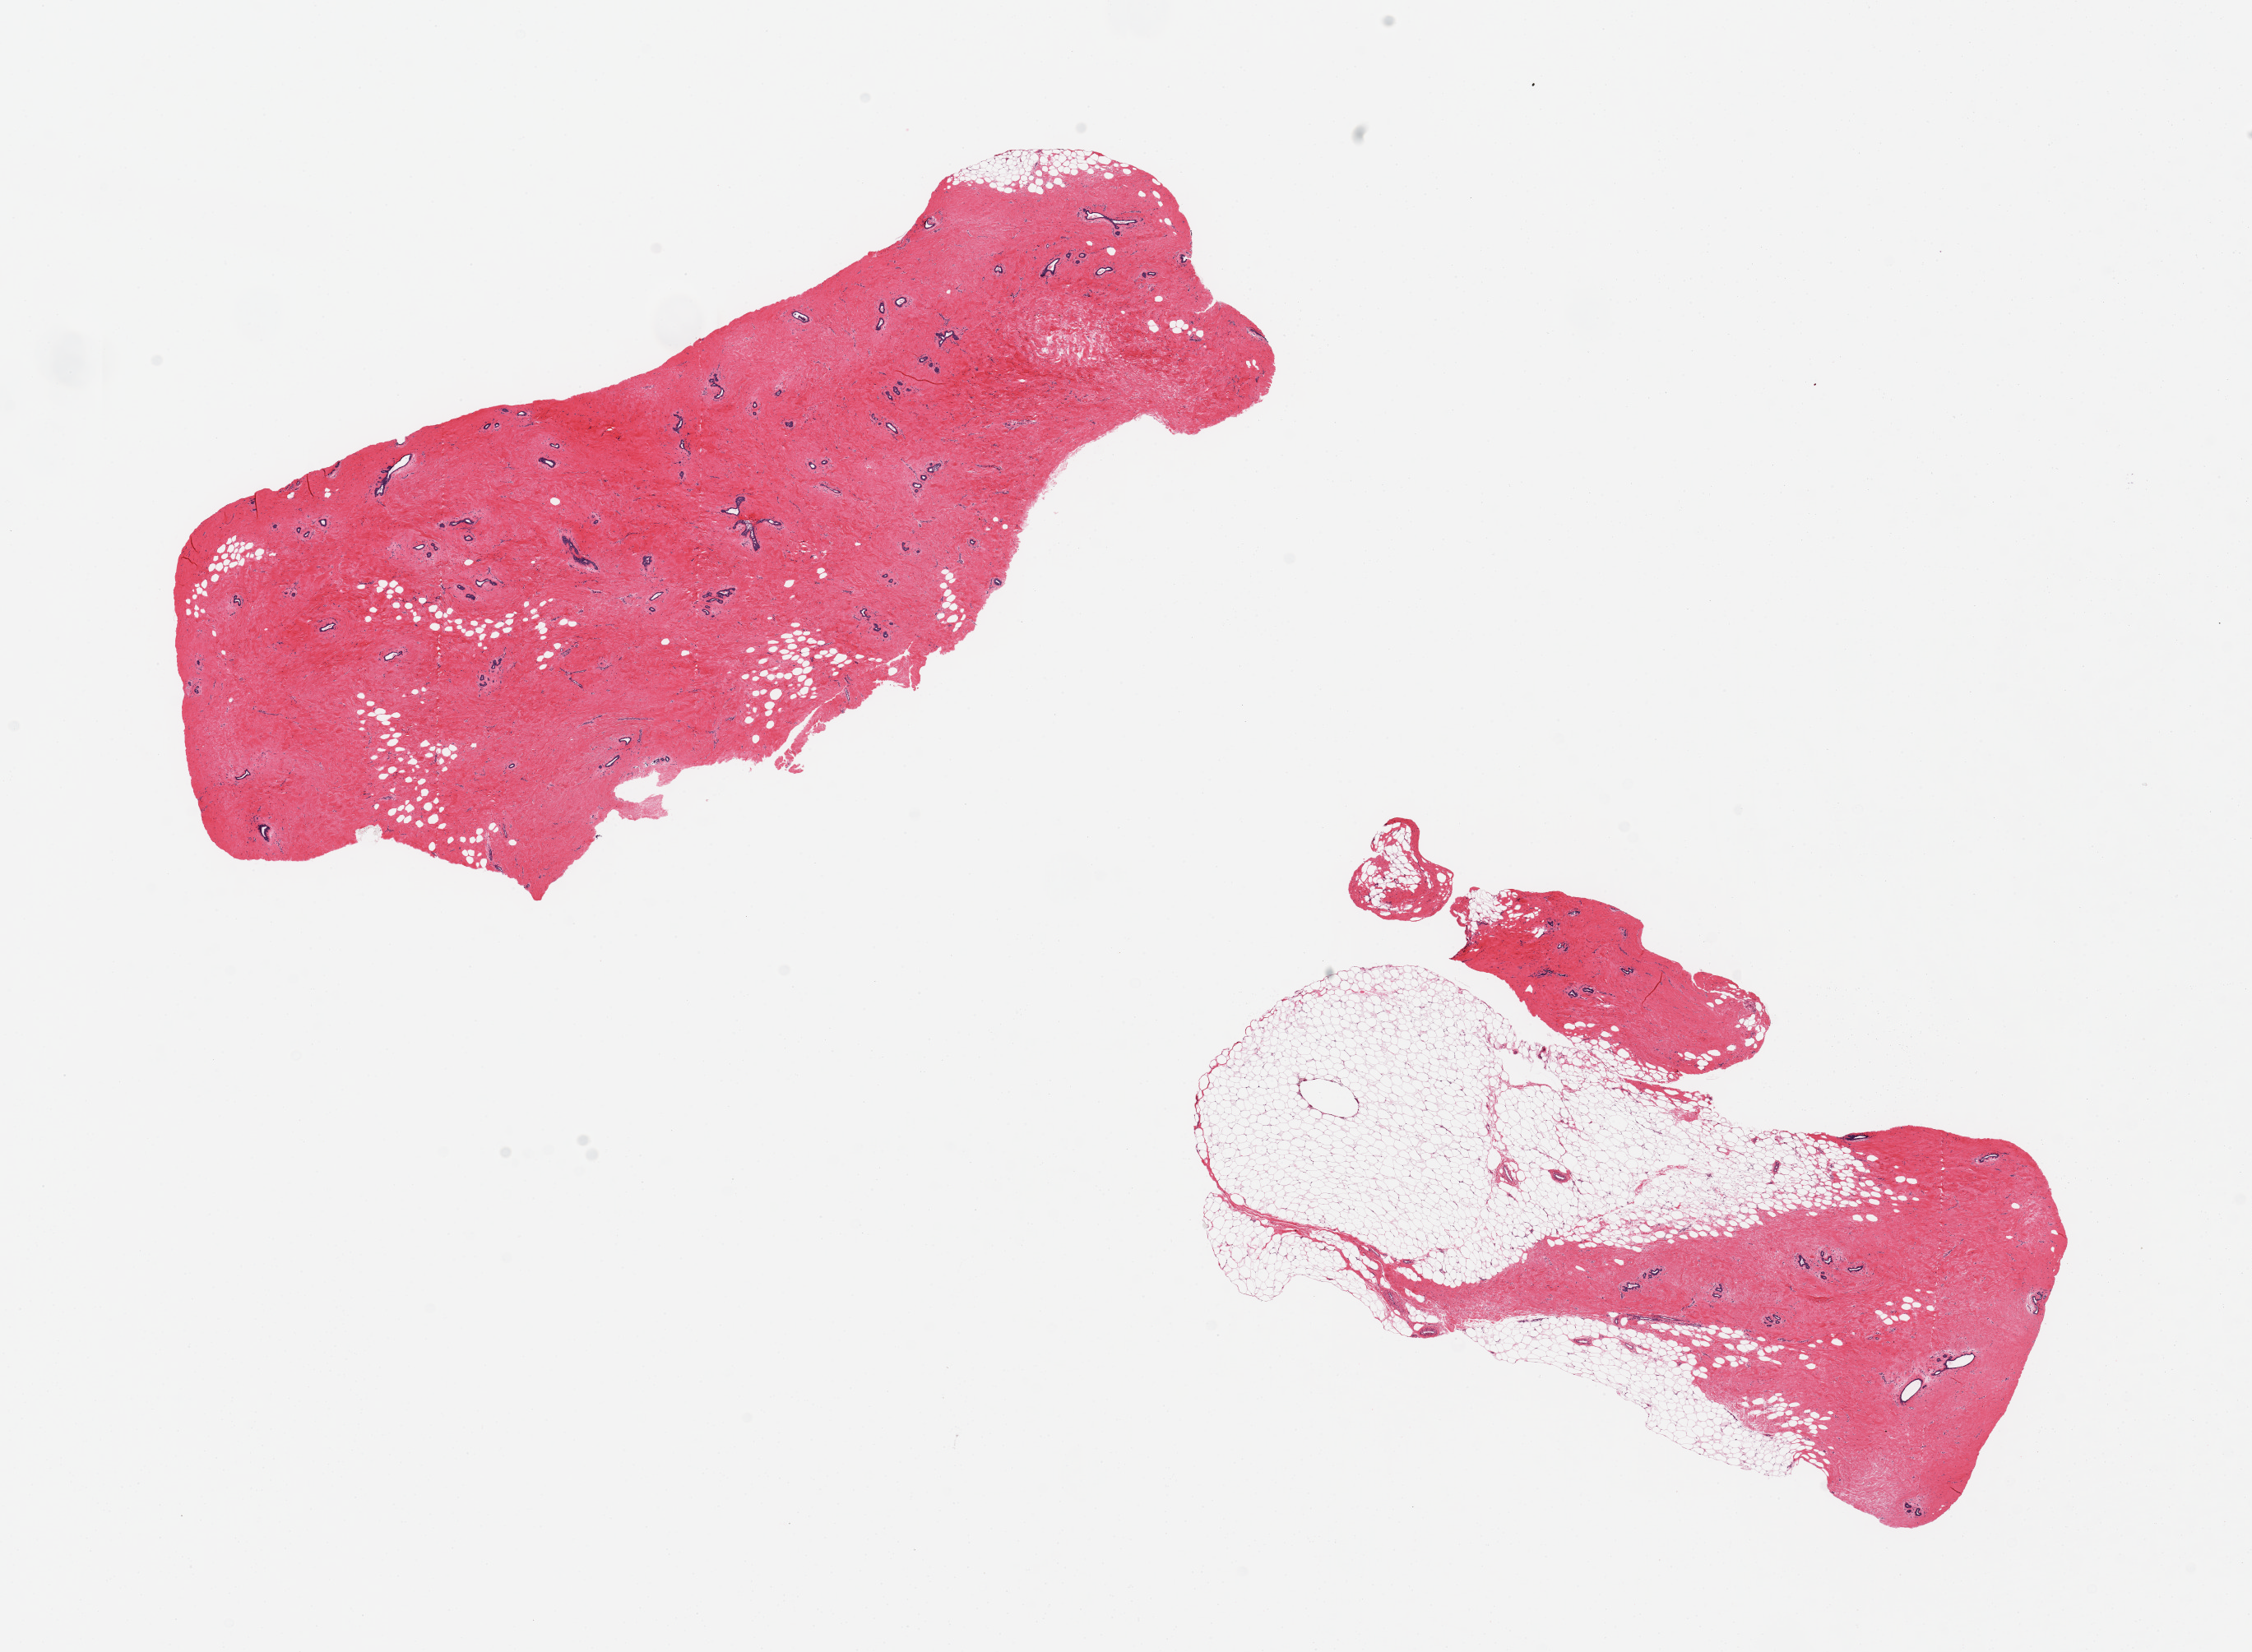
Whole-slide image, haematoxylin and eosin stain, brightfield — a low-resolution overview of the entire scanned area, about 21.7 x 15.9 mm (from a 20x scan). PAXgene-fixed paraffin-embedded (PFPE) section. Sampled site (target tissue): breast. Tissue donor sample. Donor: male.
Reviewer comment on this tissue sample: 2 pieces; fibrovascular tissue with ductal structures: gynecomastoid changes.